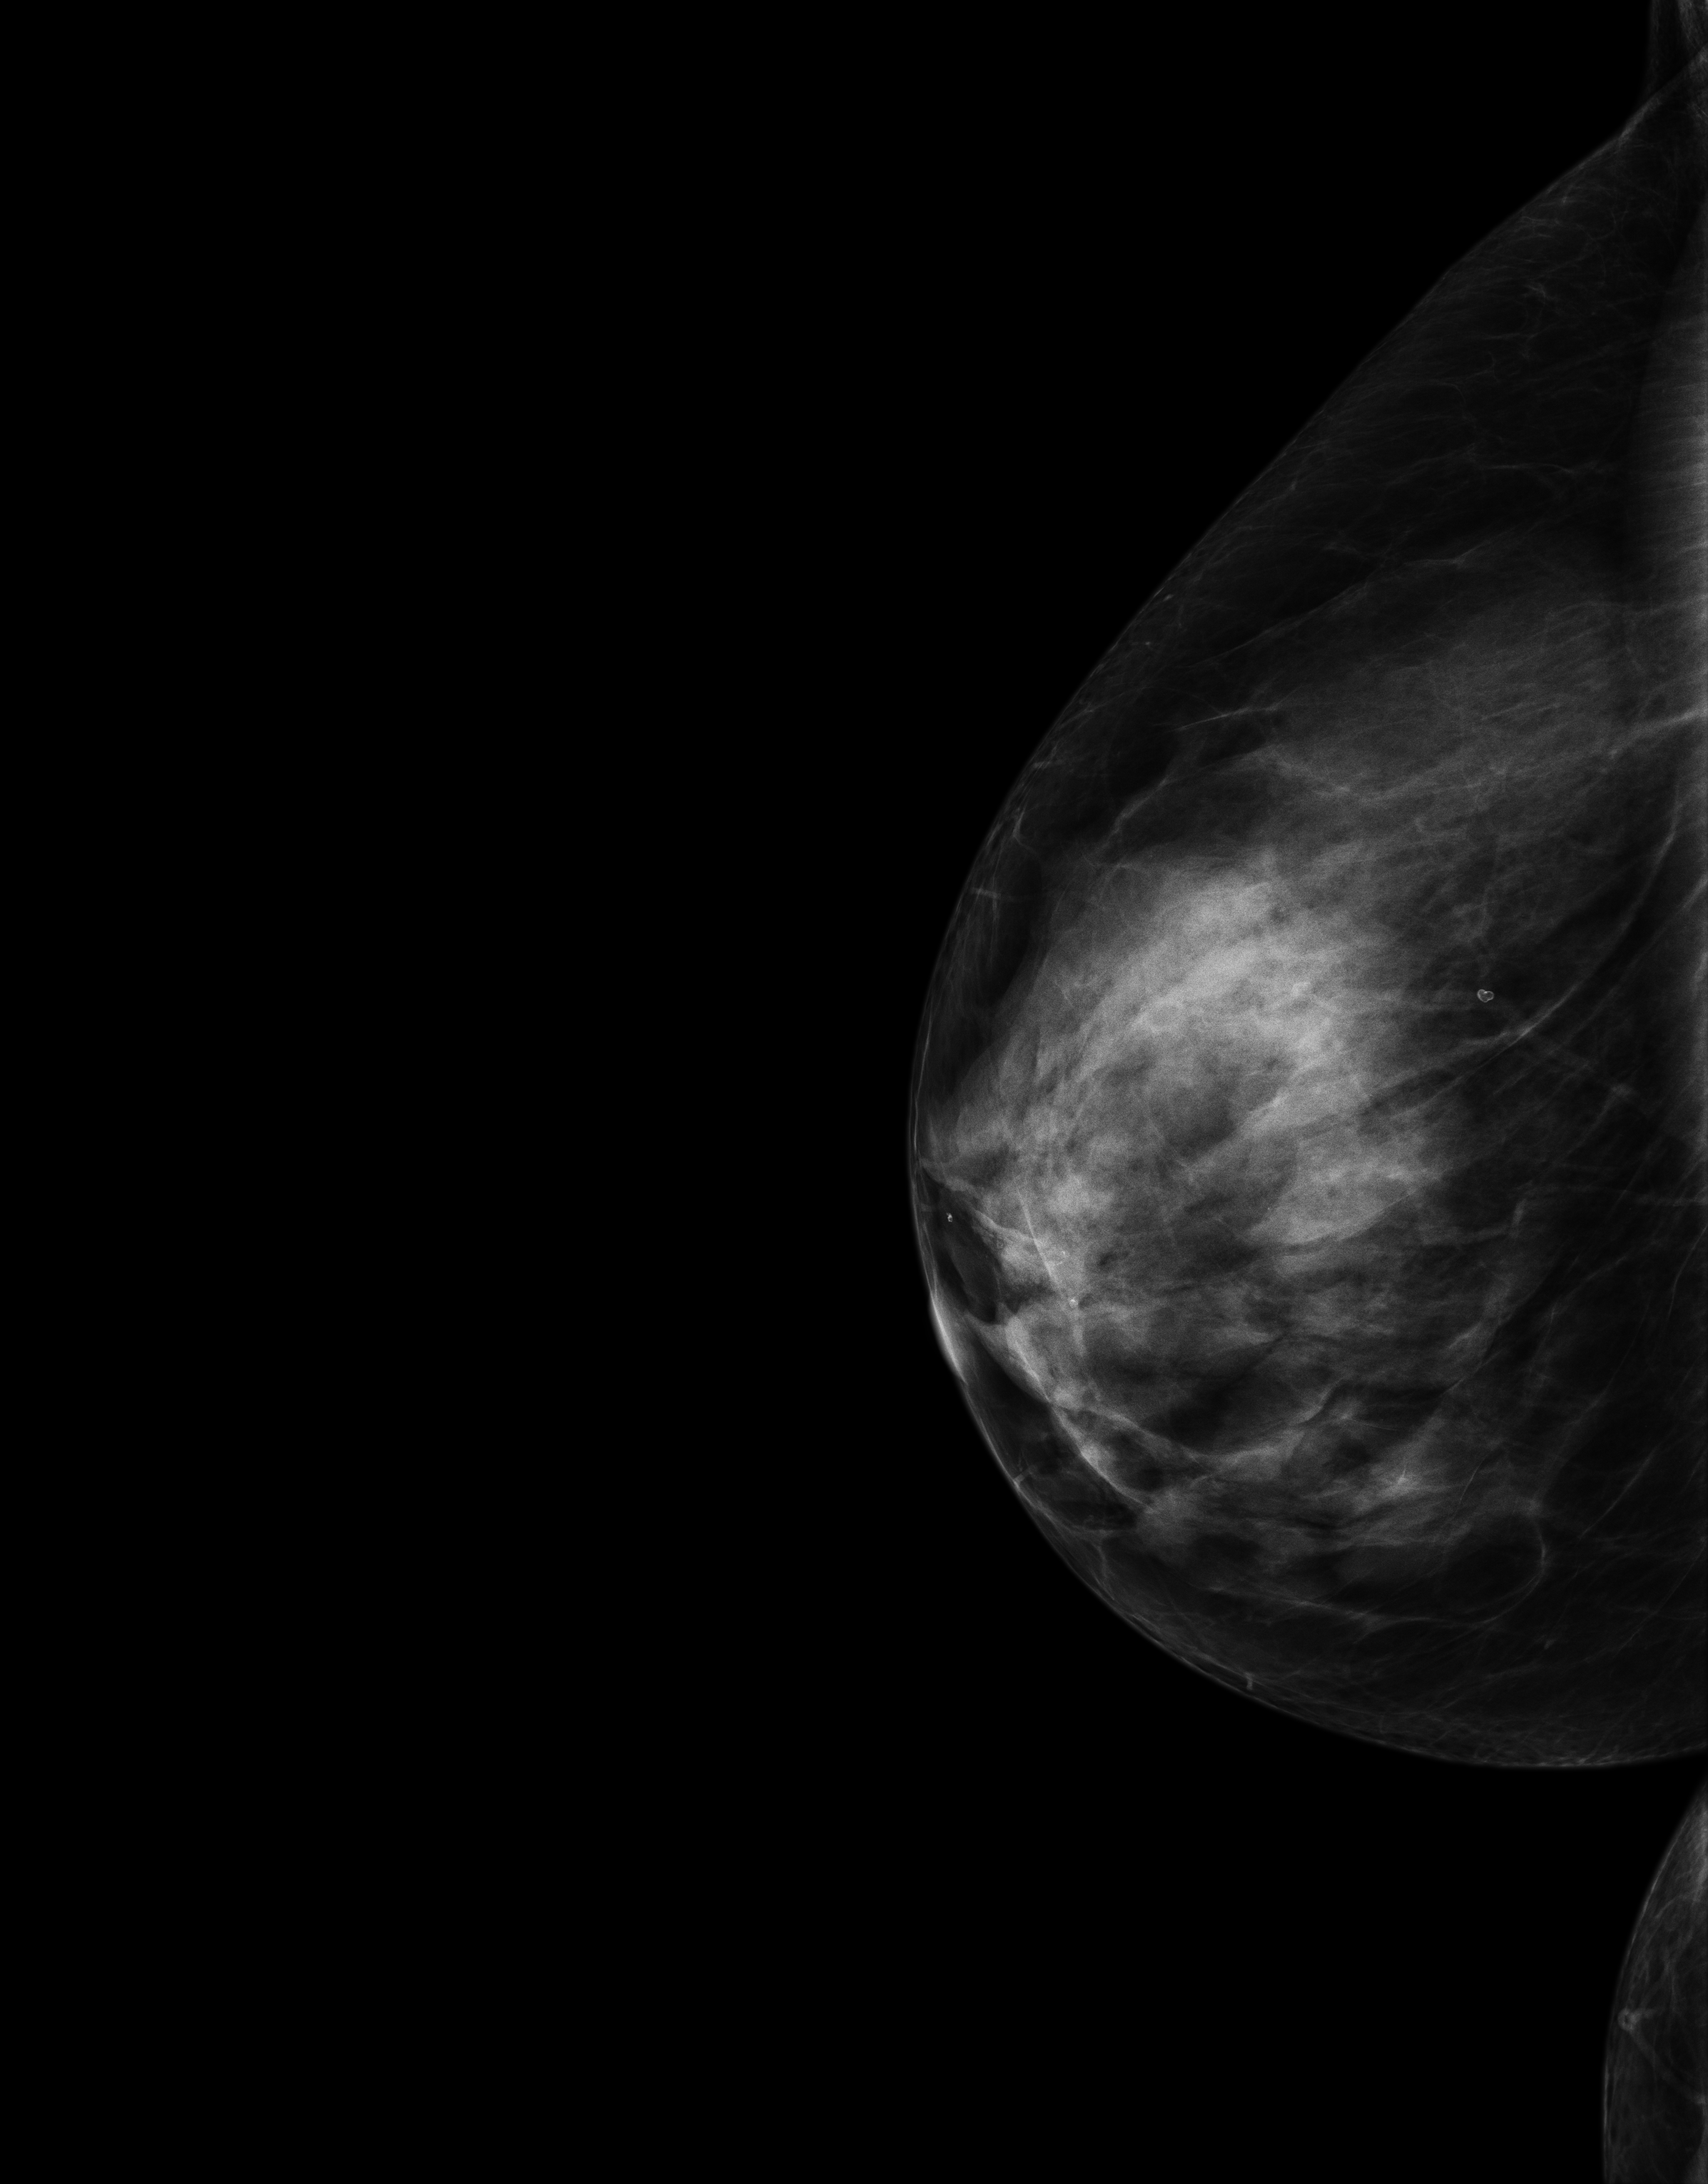
Digital mammogram (FFDM); right breast; exaggerated CC view (lateral); screening examination; system: Senographe Essential ADS_56.21.3. Patient aged 60 years (female).
BI-RADS breast density category at the screening exam (both breasts, scale 1–4): 4. Final BI-RADS category for the screening round (tomosynthesis exam, both breasts): category 1. Recall: no recall after this screen.